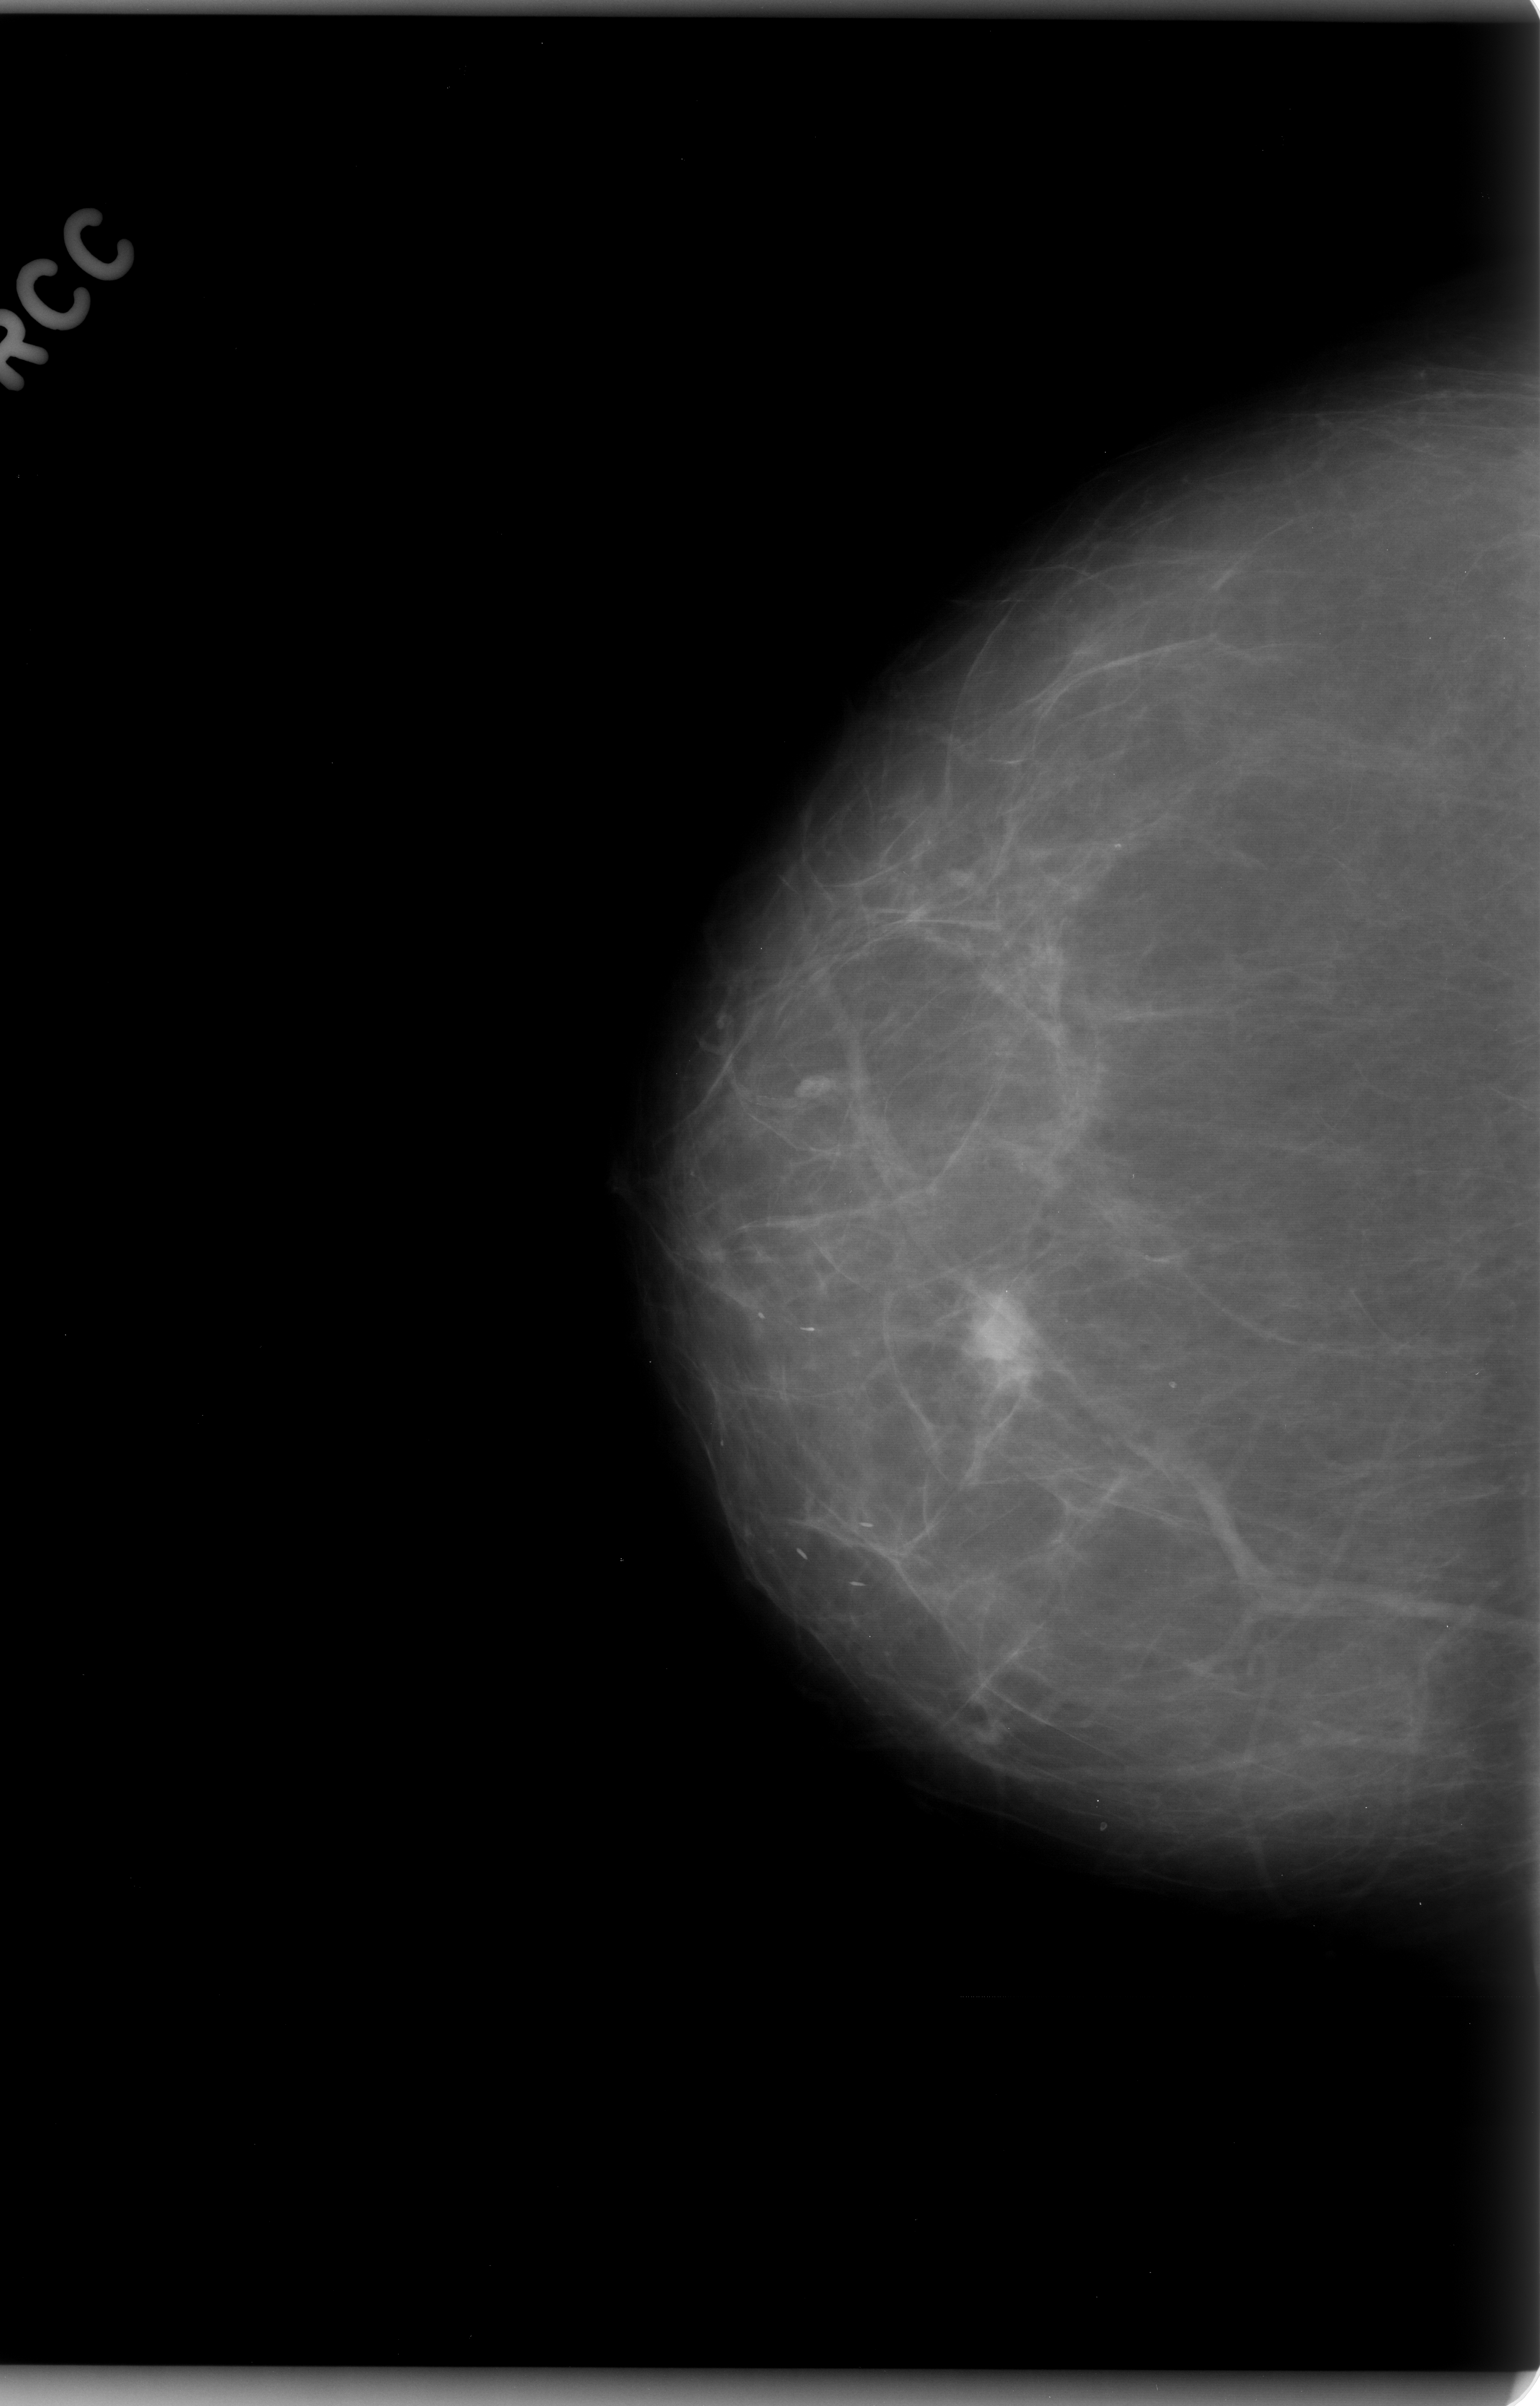
Scanned film-screen mammogram; right breast; CC view.
- Mass, shape lobulated, margins microlobulated; BI-RADS assessment category 5; subtlety rating 5 on a 1 (subtle) to 5 (obvious) scale; pathology result (as recorded, not read from the image): malignant.